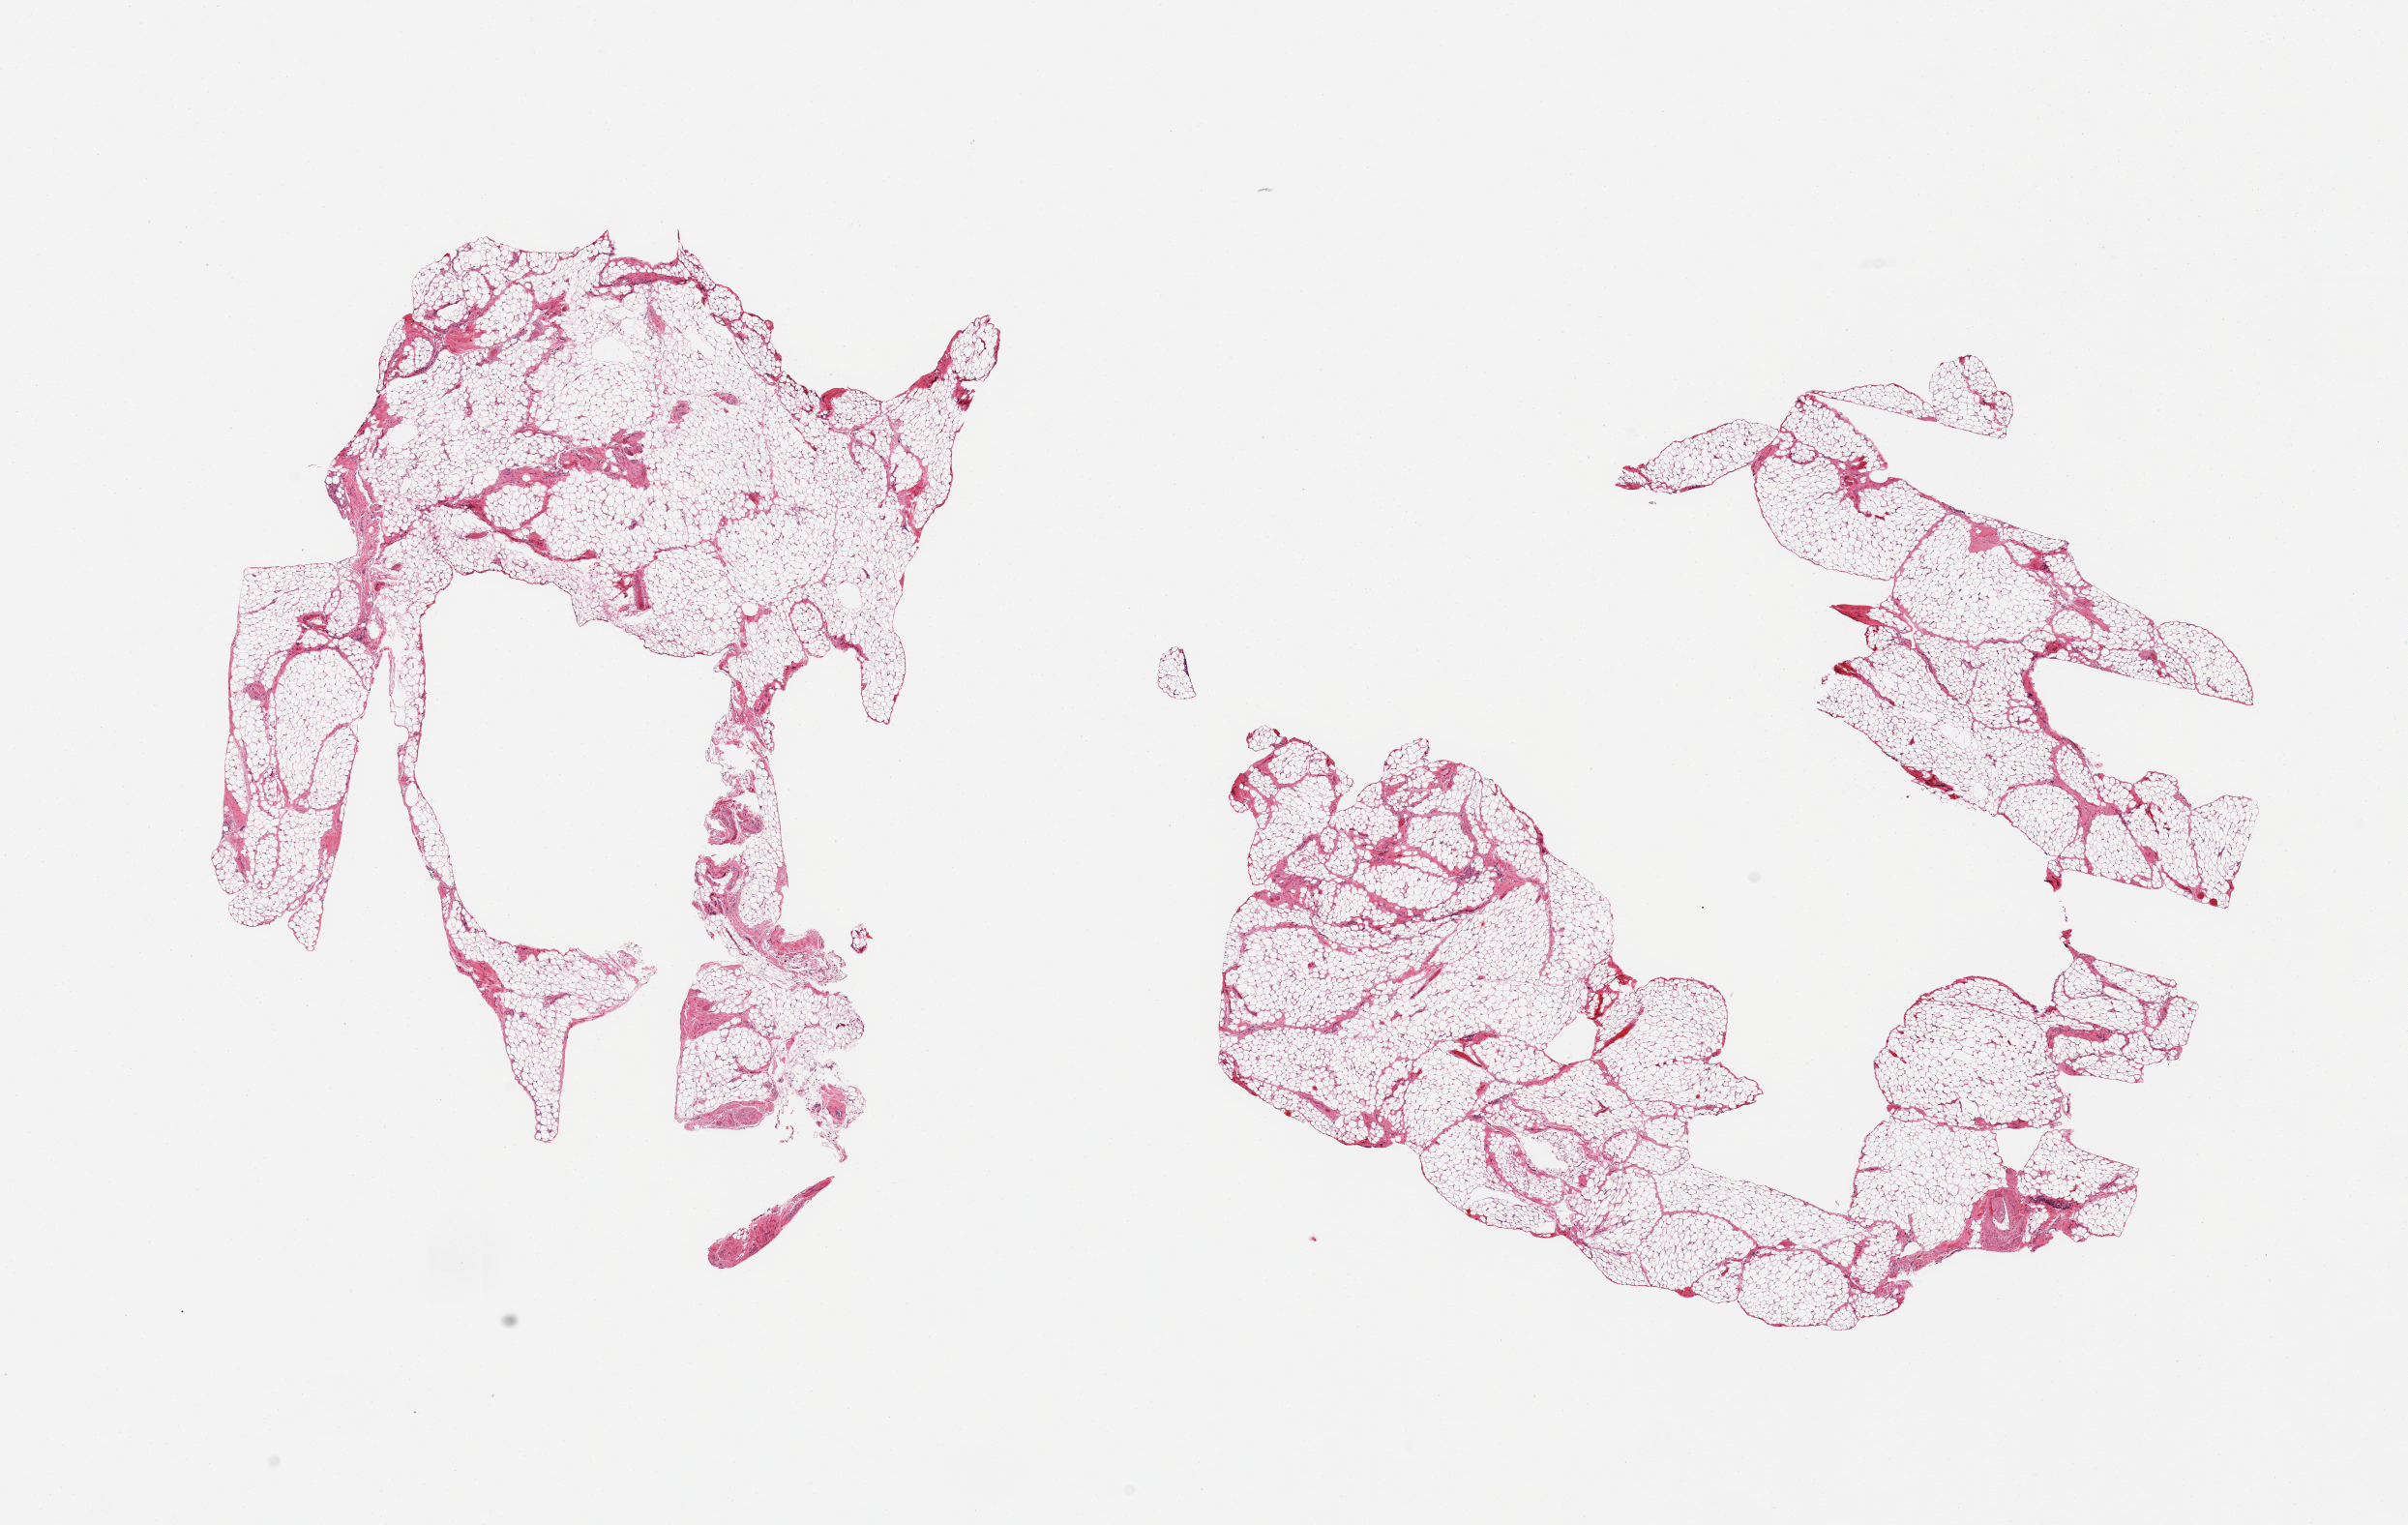
Whole-slide image, H&E stain, low-resolution overview of the scanned area, about 19.7 x 12.5 mm. PAXgene-fixed paraffin-embedded (PFPE) section. Sampled site (target tissue): omentum. Tissue donor sample. Donor: male.
Reviewer comment on this tissue sample: 2 pieces; 5% fibrous content.